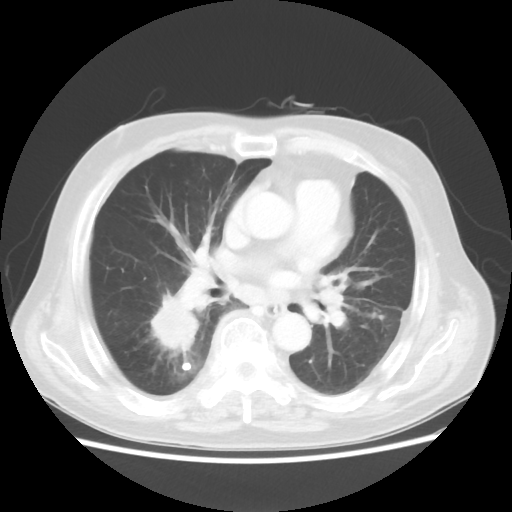
Chest CT, one axial slice. Slice 19 of 44 in the series (ordered by position). Reconstruction kernel STANDARD. Lung window (W 1500 / L -600 HU). 5 mm slice thickness. 512 × 512 image matrix, field of view 359 × 359 mm. Patient: male, 83 years. Case-level facts recorded for this patient, not image findings: clinical TNM (as recorded): T2 N3 M0.
Annotated regions visible in this slice (bounding box drawn by a radiologist):
- lung tumour (recorded histology: adenocarcinoma): bounding box <142,282,207,355> (left, top, right, bottom; pixels)